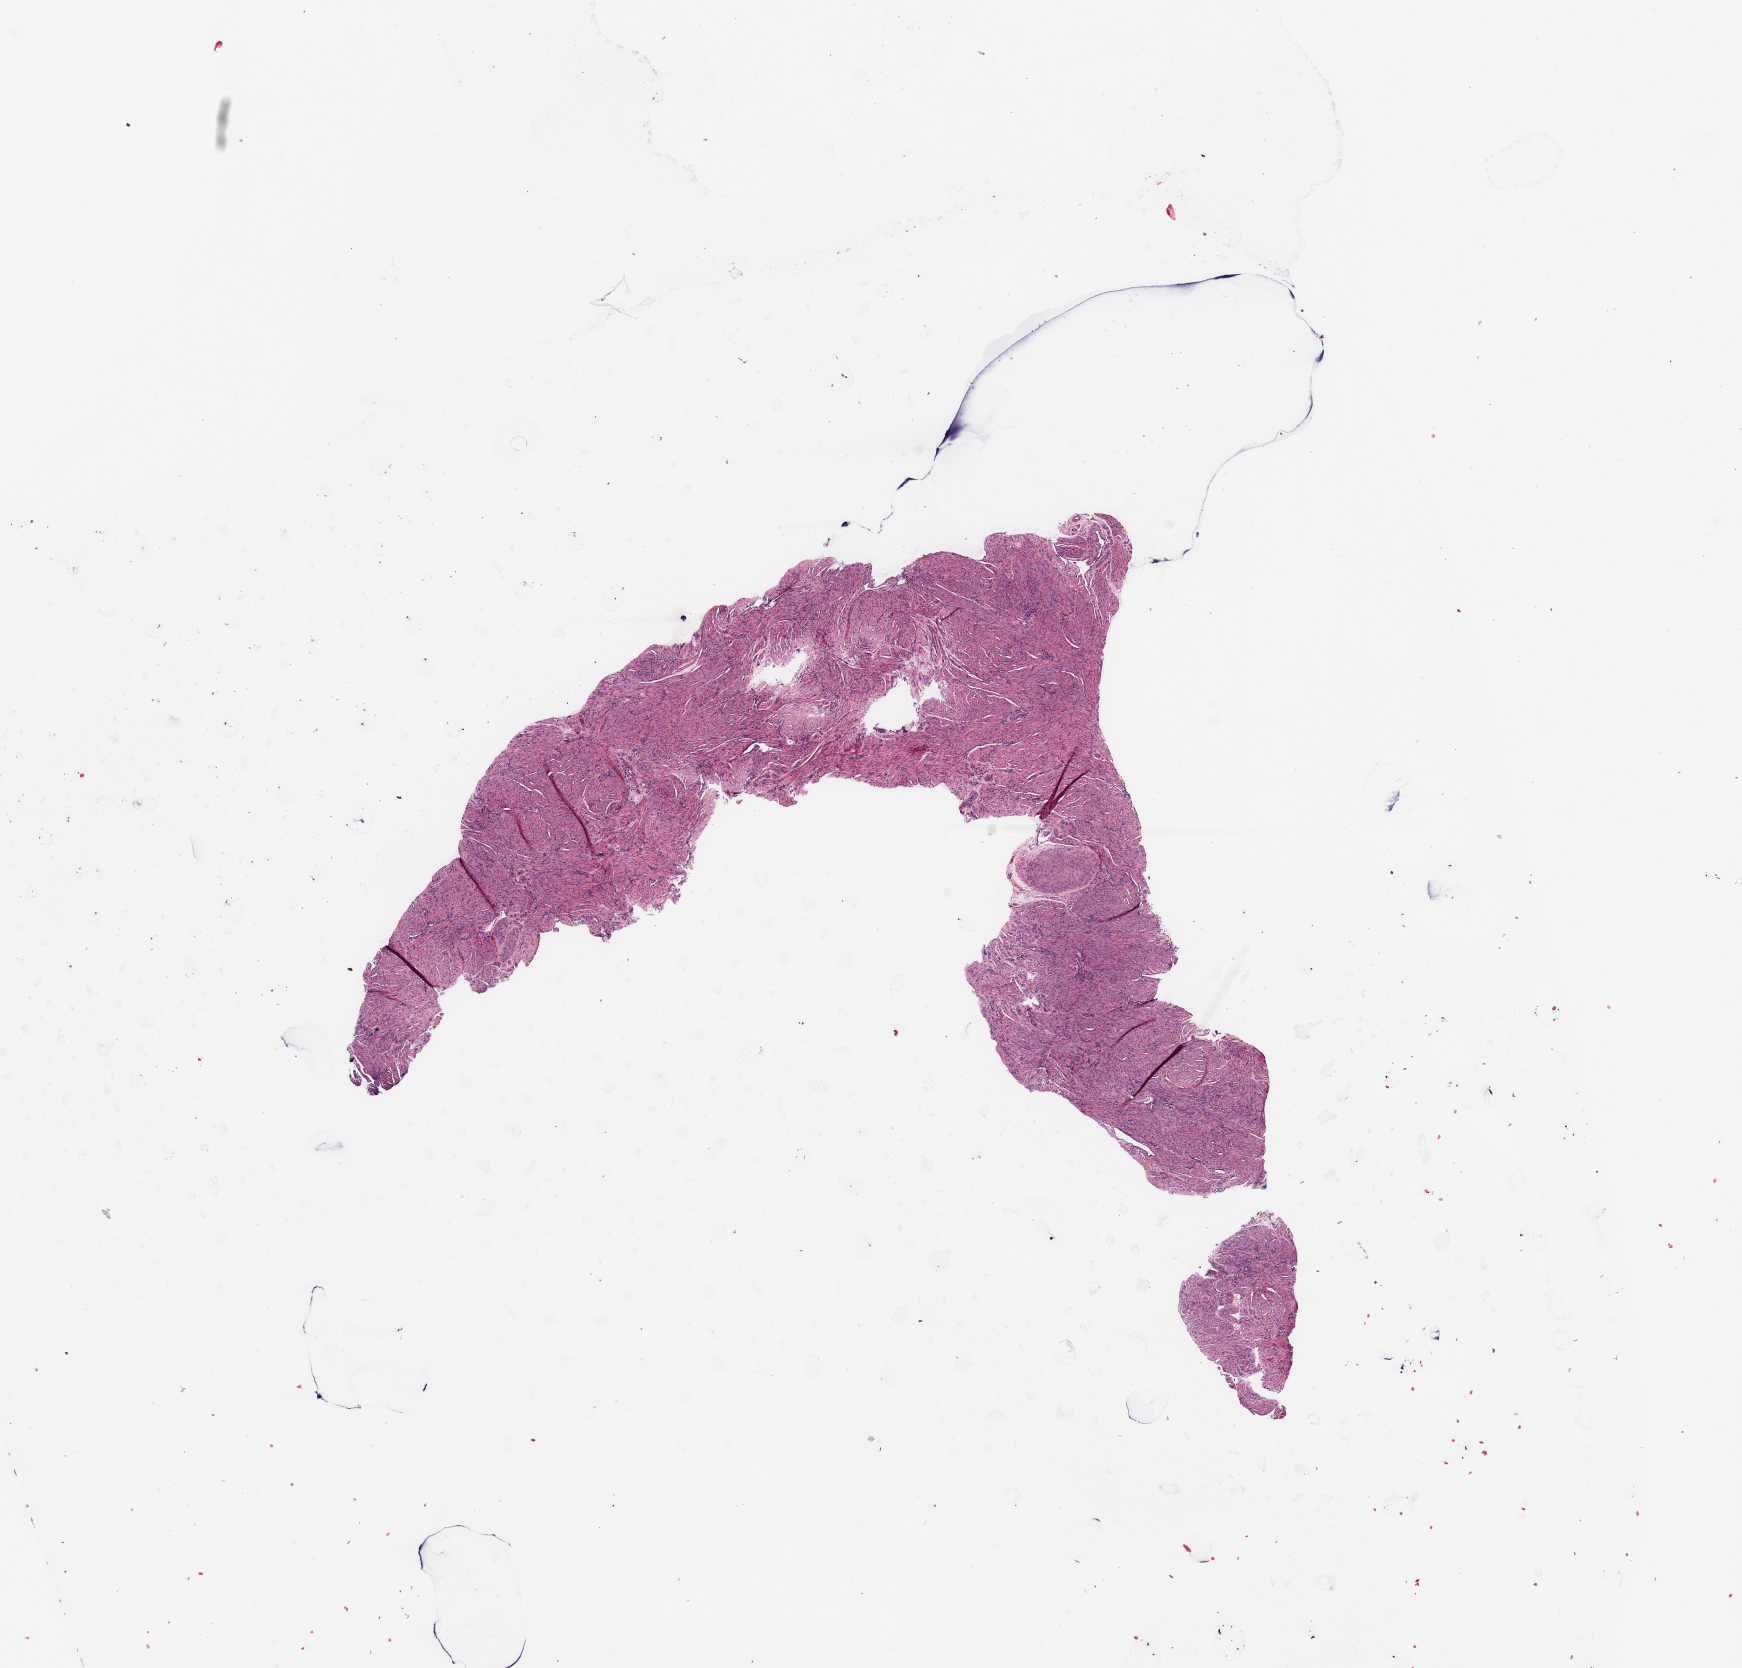
H&E whole-slide image, shown as a low-resolution overview of the whole scanned area (about 13.8 x 13.2 mm, slide scanned at 20x), uterus, normal (non-tumour) tissue. Patient: female, age 37 years.
• this section: normal (non-tumour) tissue from the same patient
• patient diagnosis: Endometrioid adenocarcinoma, NOS